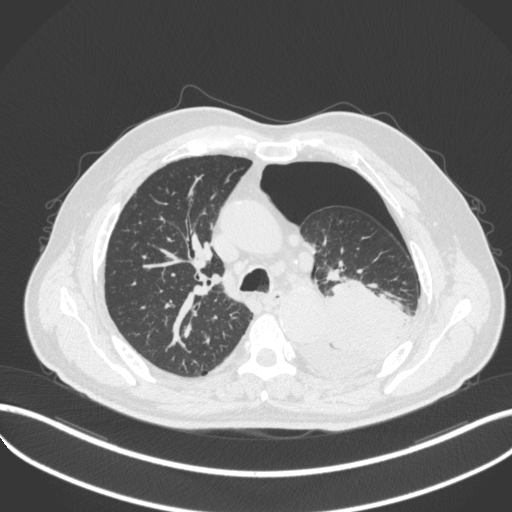
Chest CT, one axial slice. Position 351 of 466 along the scan axis. Reconstruction kernel B31f. Lung window (W 1500 / L -600 HU). 1 mm slice thickness. 512 × 512 image matrix, field of view 400 × 400 mm. Male patient, age 76 years. Case-level facts recorded for this patient, not image findings: clinical TNM (as recorded): T3 N0 M1b.
Structures marked on this image (rectangle marked by the reading radiologist):
- lung tumour (recorded histology: adenocarcinoma): box from (x=300, y=280) to (x=421, y=383) px